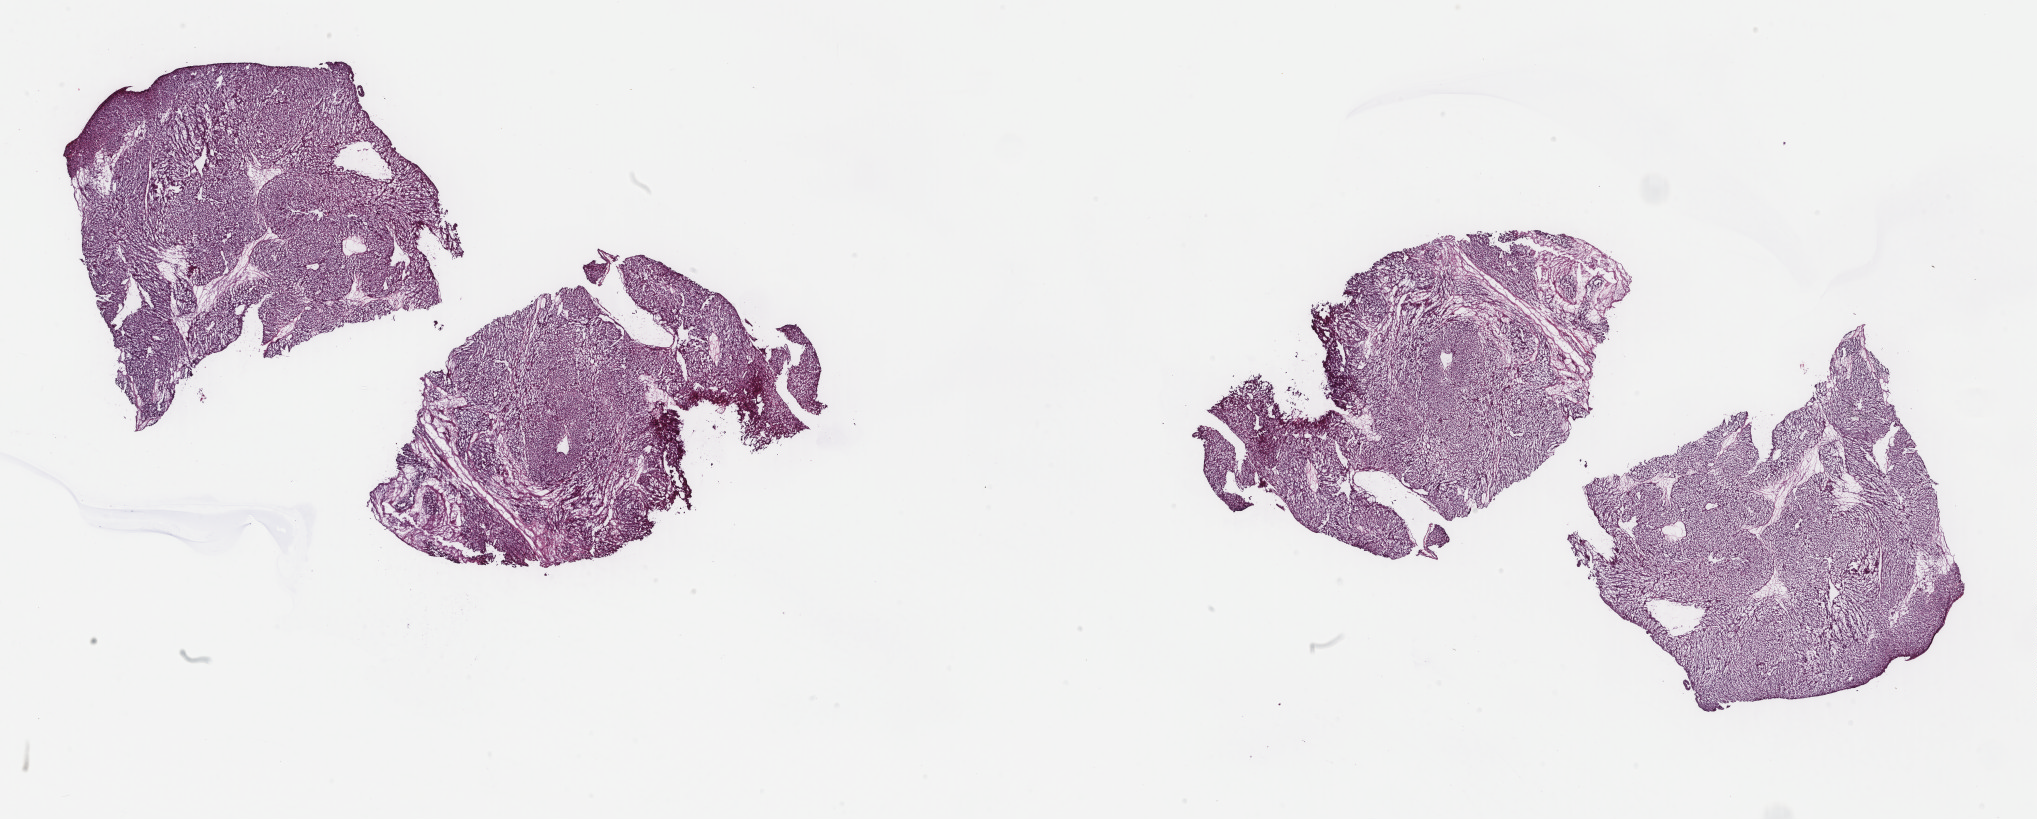
Whole-slide histology image, H&E-stained, a low-resolution overview of the entire scanned area, about 32.3 x 13.0 mm, frozen section from the top of the tissue portion, sample: primary tumour, retroperitoneum and peritoneum. Patient: male, age at initial diagnosis 56 years. Composition of this section per pathologist review: tumour cells 100%, tumour nuclei 90%.
Diagnosis: Leiomyosarcoma, NOS (retroperitoneum).